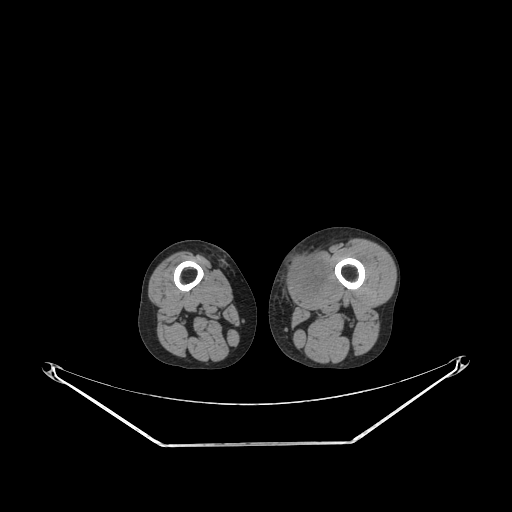
CT of an extremity soft-tissue mass (from a PET/CT study), one axial slice; position 211 of 267 along the scan axis; reconstruction kernel STANDARD; 140 kVp; soft-tissue window (W 400 / L 40 HU); 512 × 512 image matrix, field of view 500 × 500 mm. Male patient. Case-level facts recorded for this patient, not image findings: histological type: pleiomorphic leiomyosarcoma; grade: high; site of the primary tumour: left thigh.
Outlined on this slice (expert contour drawn on MRI and transferred to this co-registered scan by the dataset authors):
- gross tumour volume including surrounding oedema: bounding box (x1, y1, x2, y2) in pixels: (285, 253, 328, 302)
- gross tumour volume (mass): (285, 253, 325, 295)